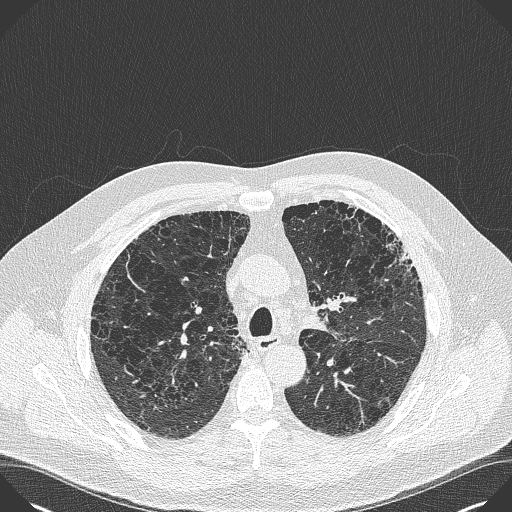
Axial slice from a low-dose chest CT screening exam. Baseline annual screen. Lung window (W 1500 / L -600 HU). 1 mm slice thickness. 120 kVp. Slice 127 of 383 in the series. Male participant, aged 59 years at enrolment.
Expert reader's lesion annotation, bounding box (x1, y1, x2, y2) in pixels: (376, 233, 427, 285). Screening reader's record for this exam: no non-calcified nodule ≥4 mm recorded. Official screen result: negative screen, minor abnormalities not suspicious for lung cancer. Later outcome: lung cancer diagnosed 909 days after this screen — bronchiolo-alveolar carcinoma, mixed mucinous and non-mucinous, left upper lobe, stage IA (AJCC 6th edition), 20 mm at pathology.